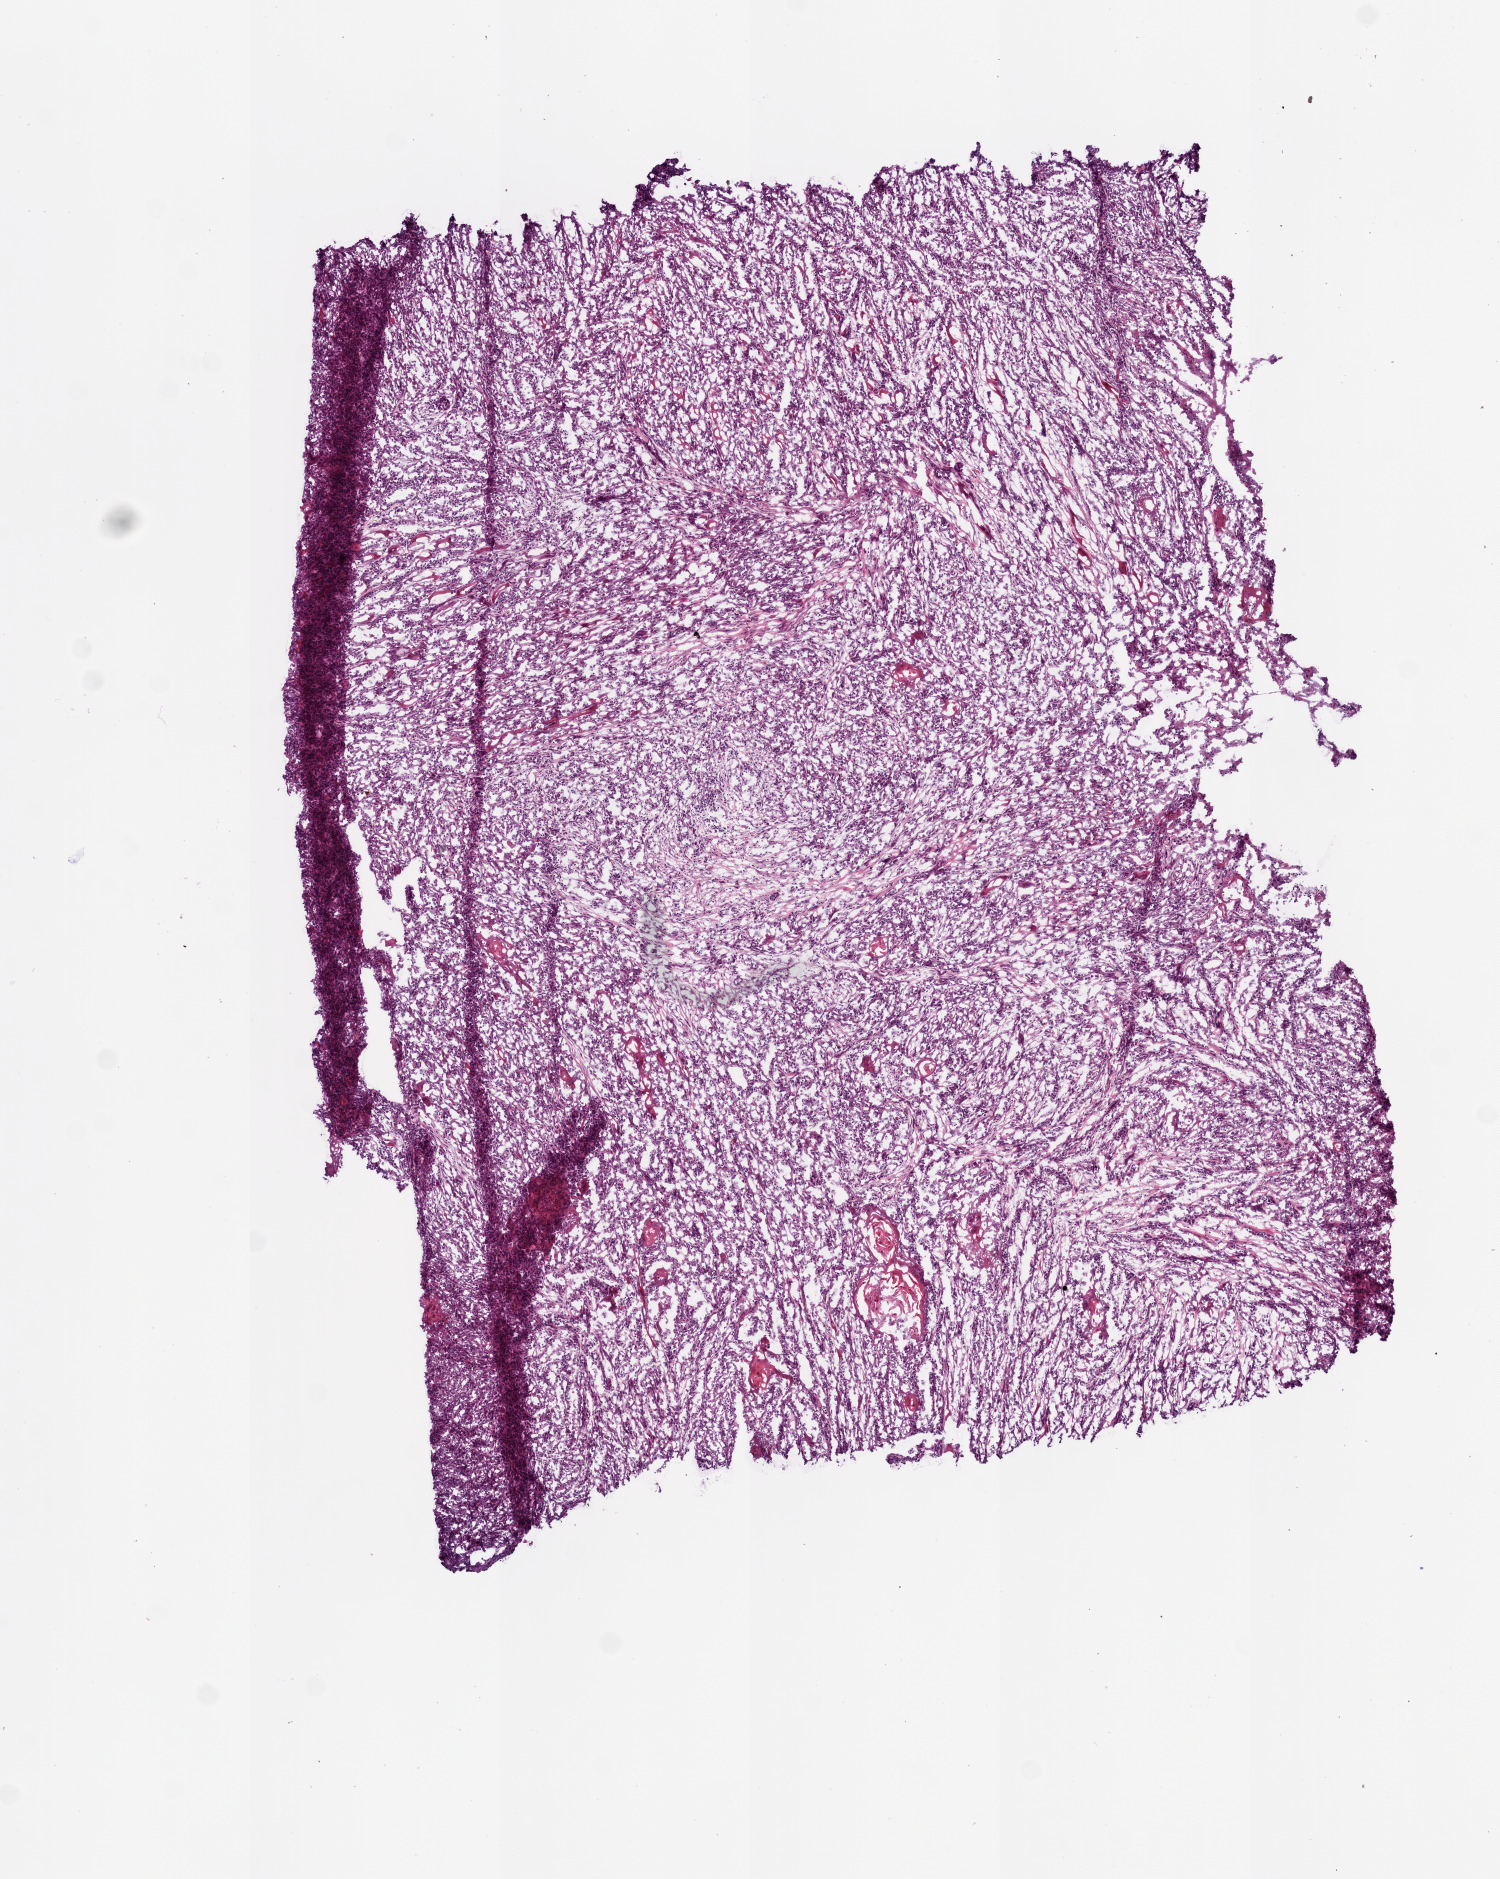
Whole-slide histology image, Hematoxylin and eosin (H&E) stained — low-resolution overview of the scanned area, about 6.0 x 7.5 mm (slide scanned at 20x); frozen section; head and neck, primary tumour sample. Patient: male, age at initial diagnosis 74 years. Histologic grade: G3 (poorly differentiated). Pathologist review of this section (percent, as recorded): tumour cells 100%, tumour nuclei 70%, necrosis 0%. Inflammatory infiltration, as recorded: lymphocyte infiltration 15%, neutrophil infiltration 2%.
AJCC pathologic stage: II (6th edition). Histologic diagnosis: Squamous cell carcinoma, NOS.